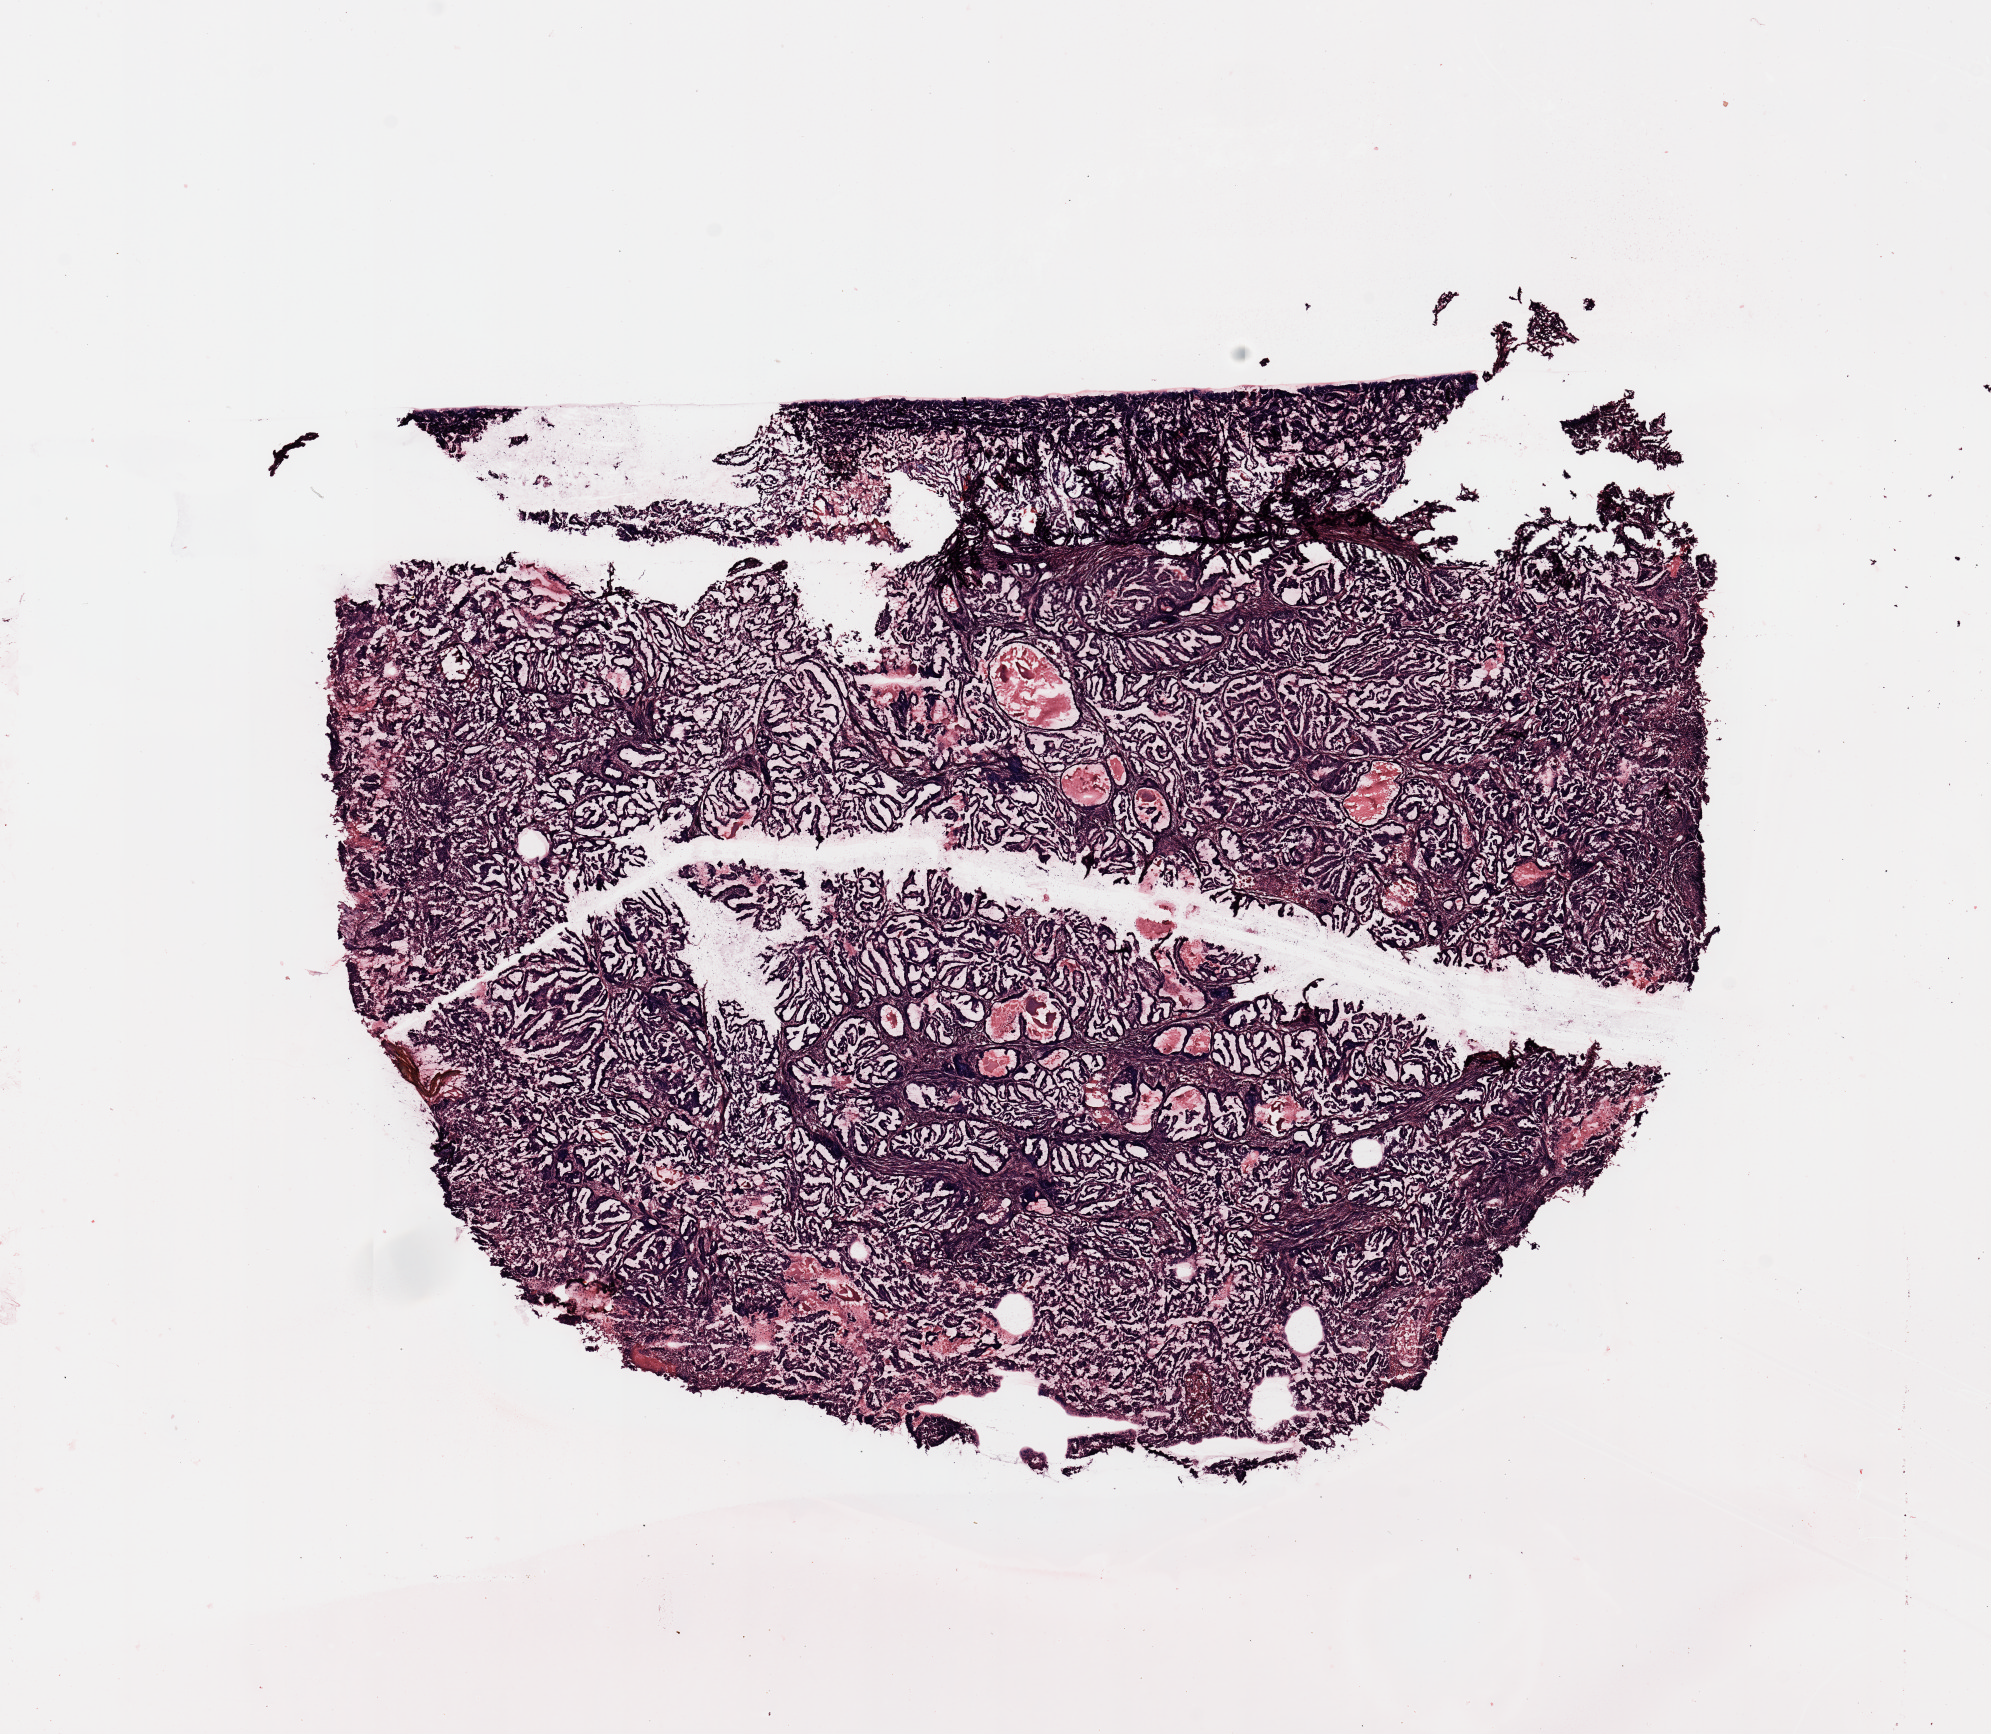
Hematoxylin and eosin (H&E) stained whole-slide image, shown as a low-resolution overview of the whole scanned area (about 15.8 x 13.7 mm, from a 20x scan); tumour tissue sample, sampled site: uterus. 70-year-old female patient. Slide review estimates, as recorded: tumour nuclei 95%, necrosis 0%.
Histologic diagnosis: Endometrioid adenocarcinoma, NOS.